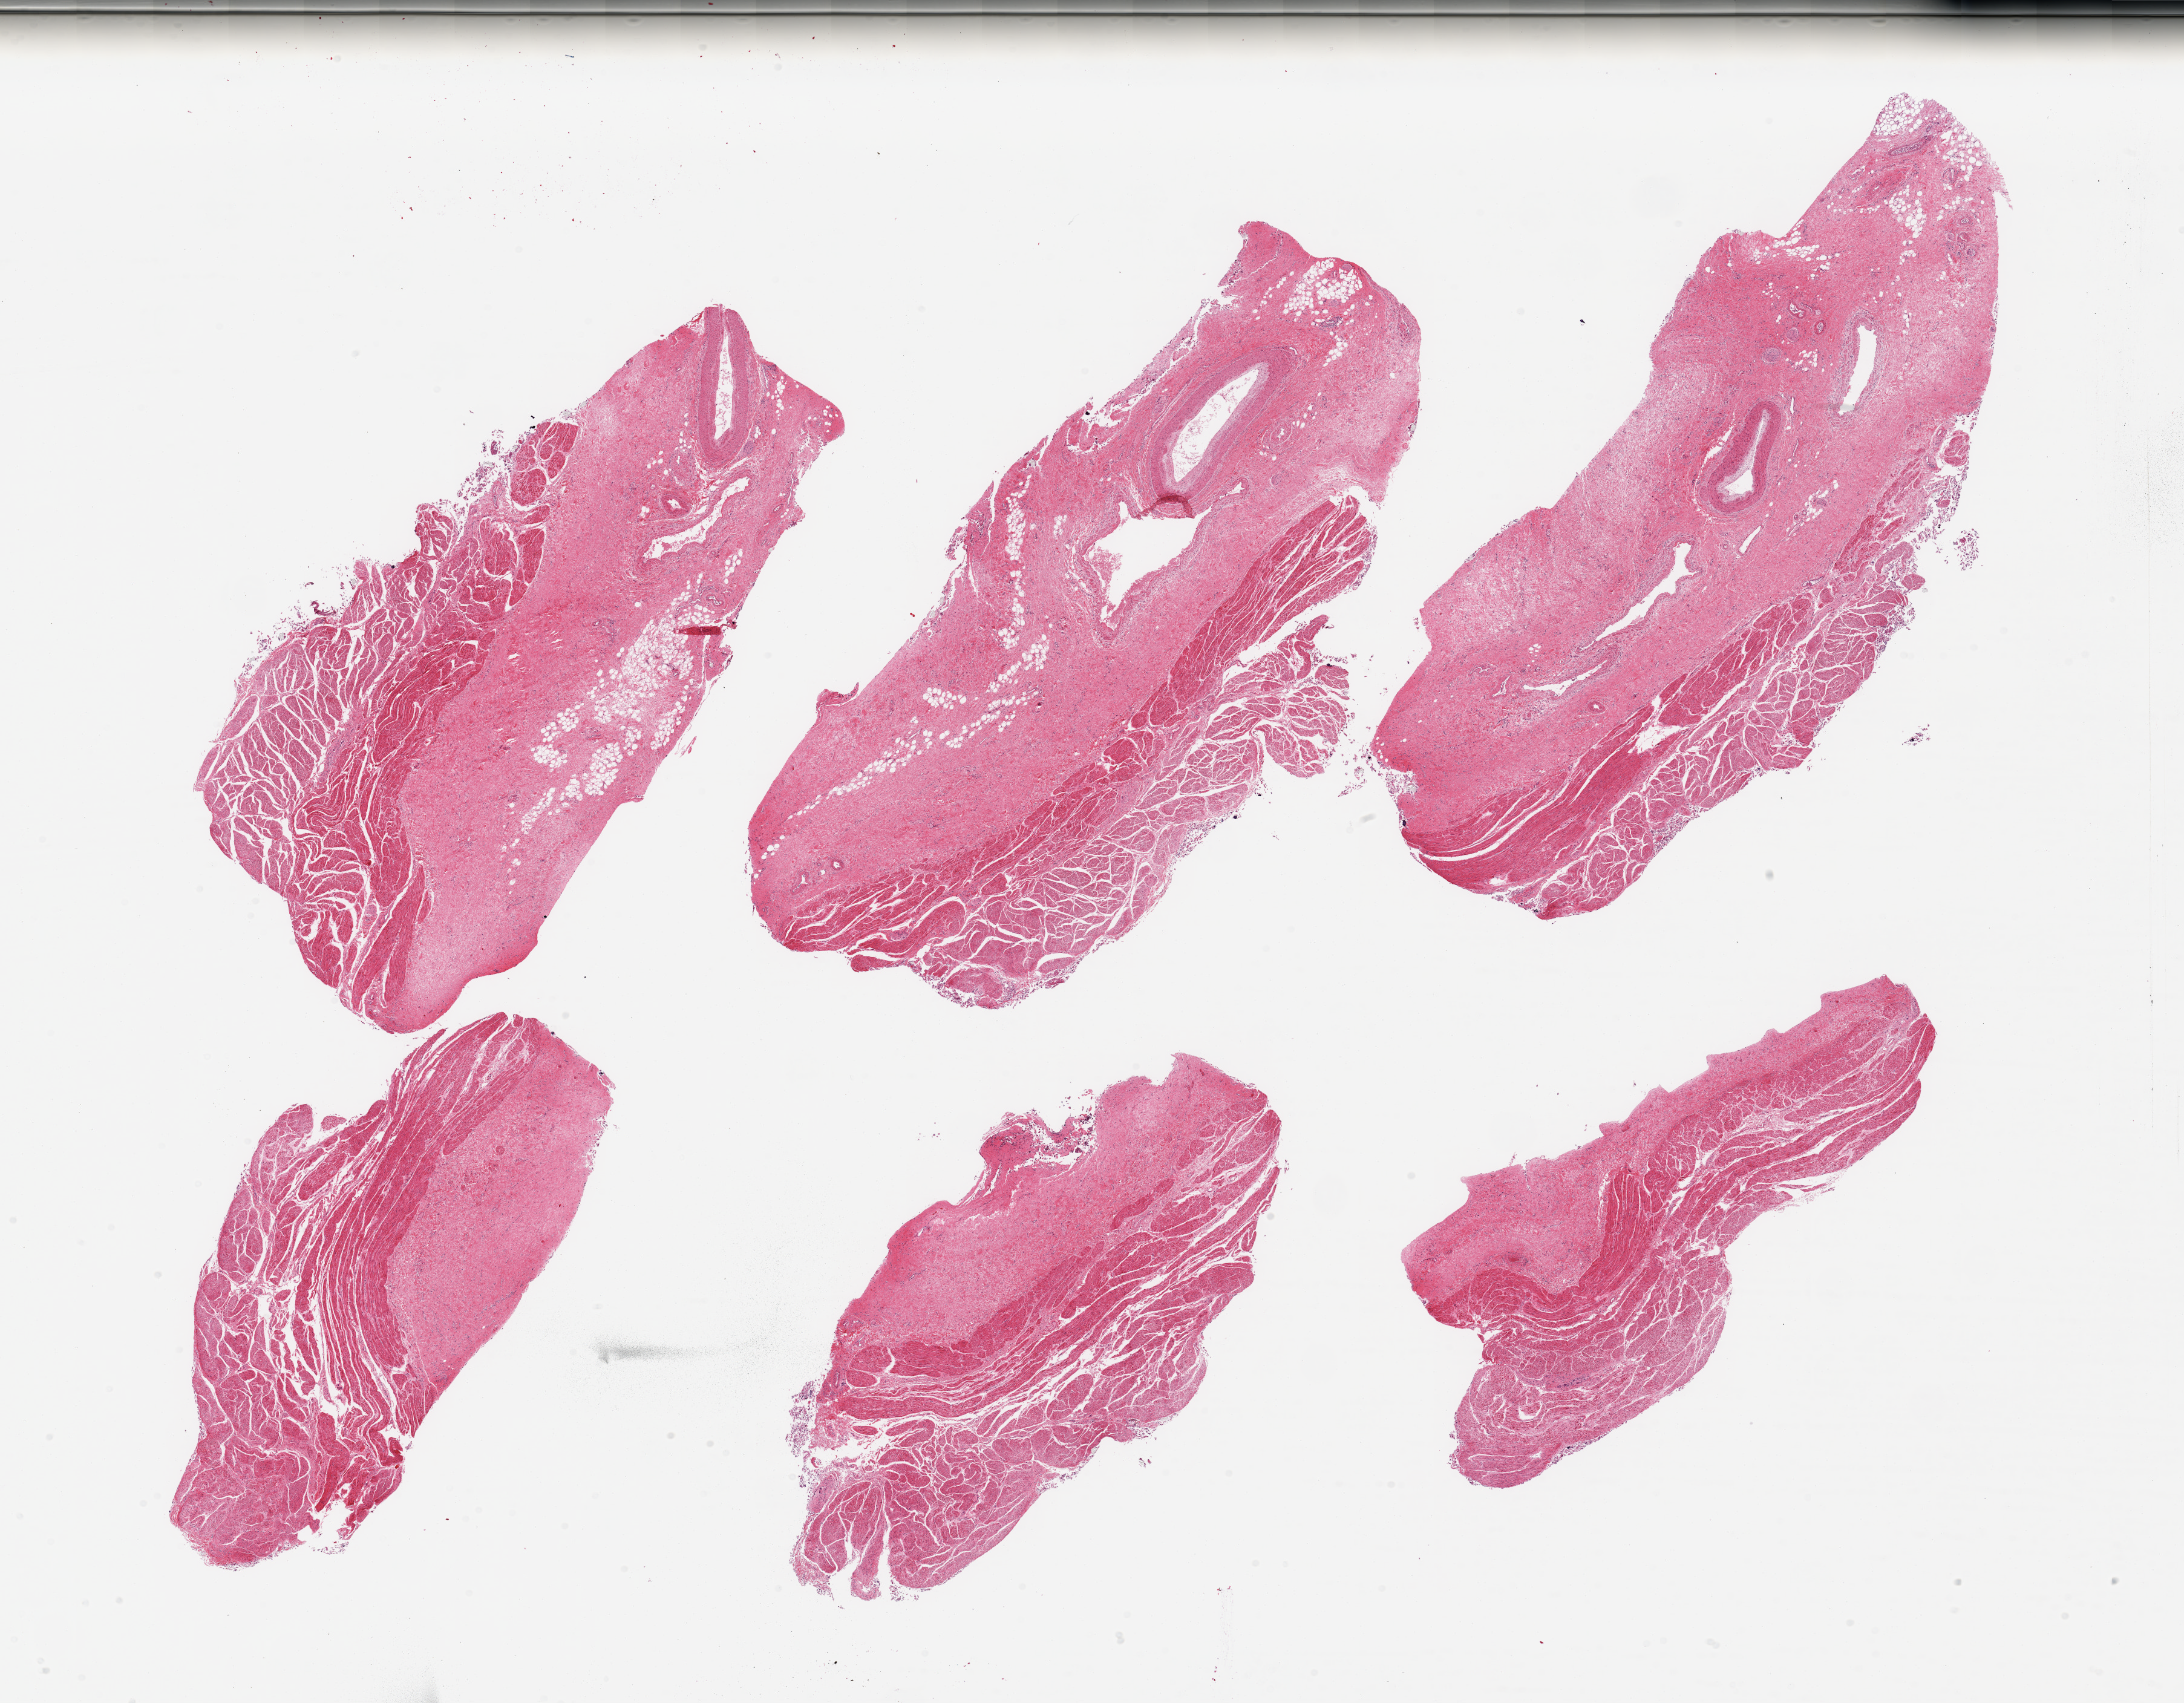
Whole-slide image, haematoxylin and eosin stain, brightfield — shown as a low-resolution overview of the whole scanned area (about 28.5 x 22.3 mm, slide scanned at 20x); PAXgene-fixed, paraffin-embedded tissue; target tissue: stomach; donor tissue sample. Male donor.
Reviewer comment on this tissue sample: 6 pieces; no mucosa, only muscle and stroma.